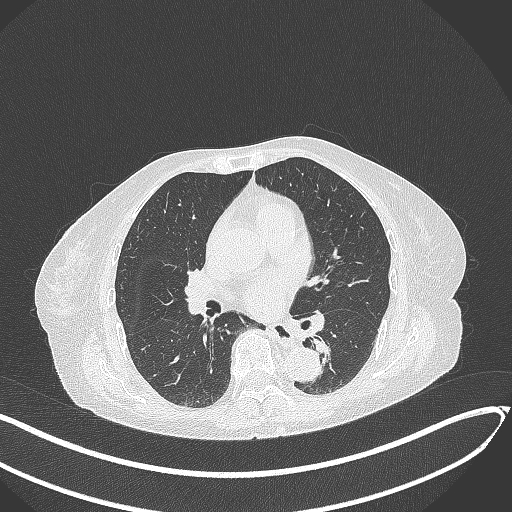
Chest CT, one axial slice; reconstruction kernel B70f; lung window (W 1500 / L -600 HU); 1 mm slice thickness; 512 × 512 image matrix, field of view 400 × 400 mm. Female patient, age 82 years. Case-level facts recorded for this patient, not image findings: clinical TNM (as recorded): T1b N0 M1.
Structures marked on this image (rectangle marked by the reading radiologist):
- lung tumour (recorded histology: adenocarcinoma): bounding box [x1, y1, x2, y2] px = [310, 334, 337, 360]